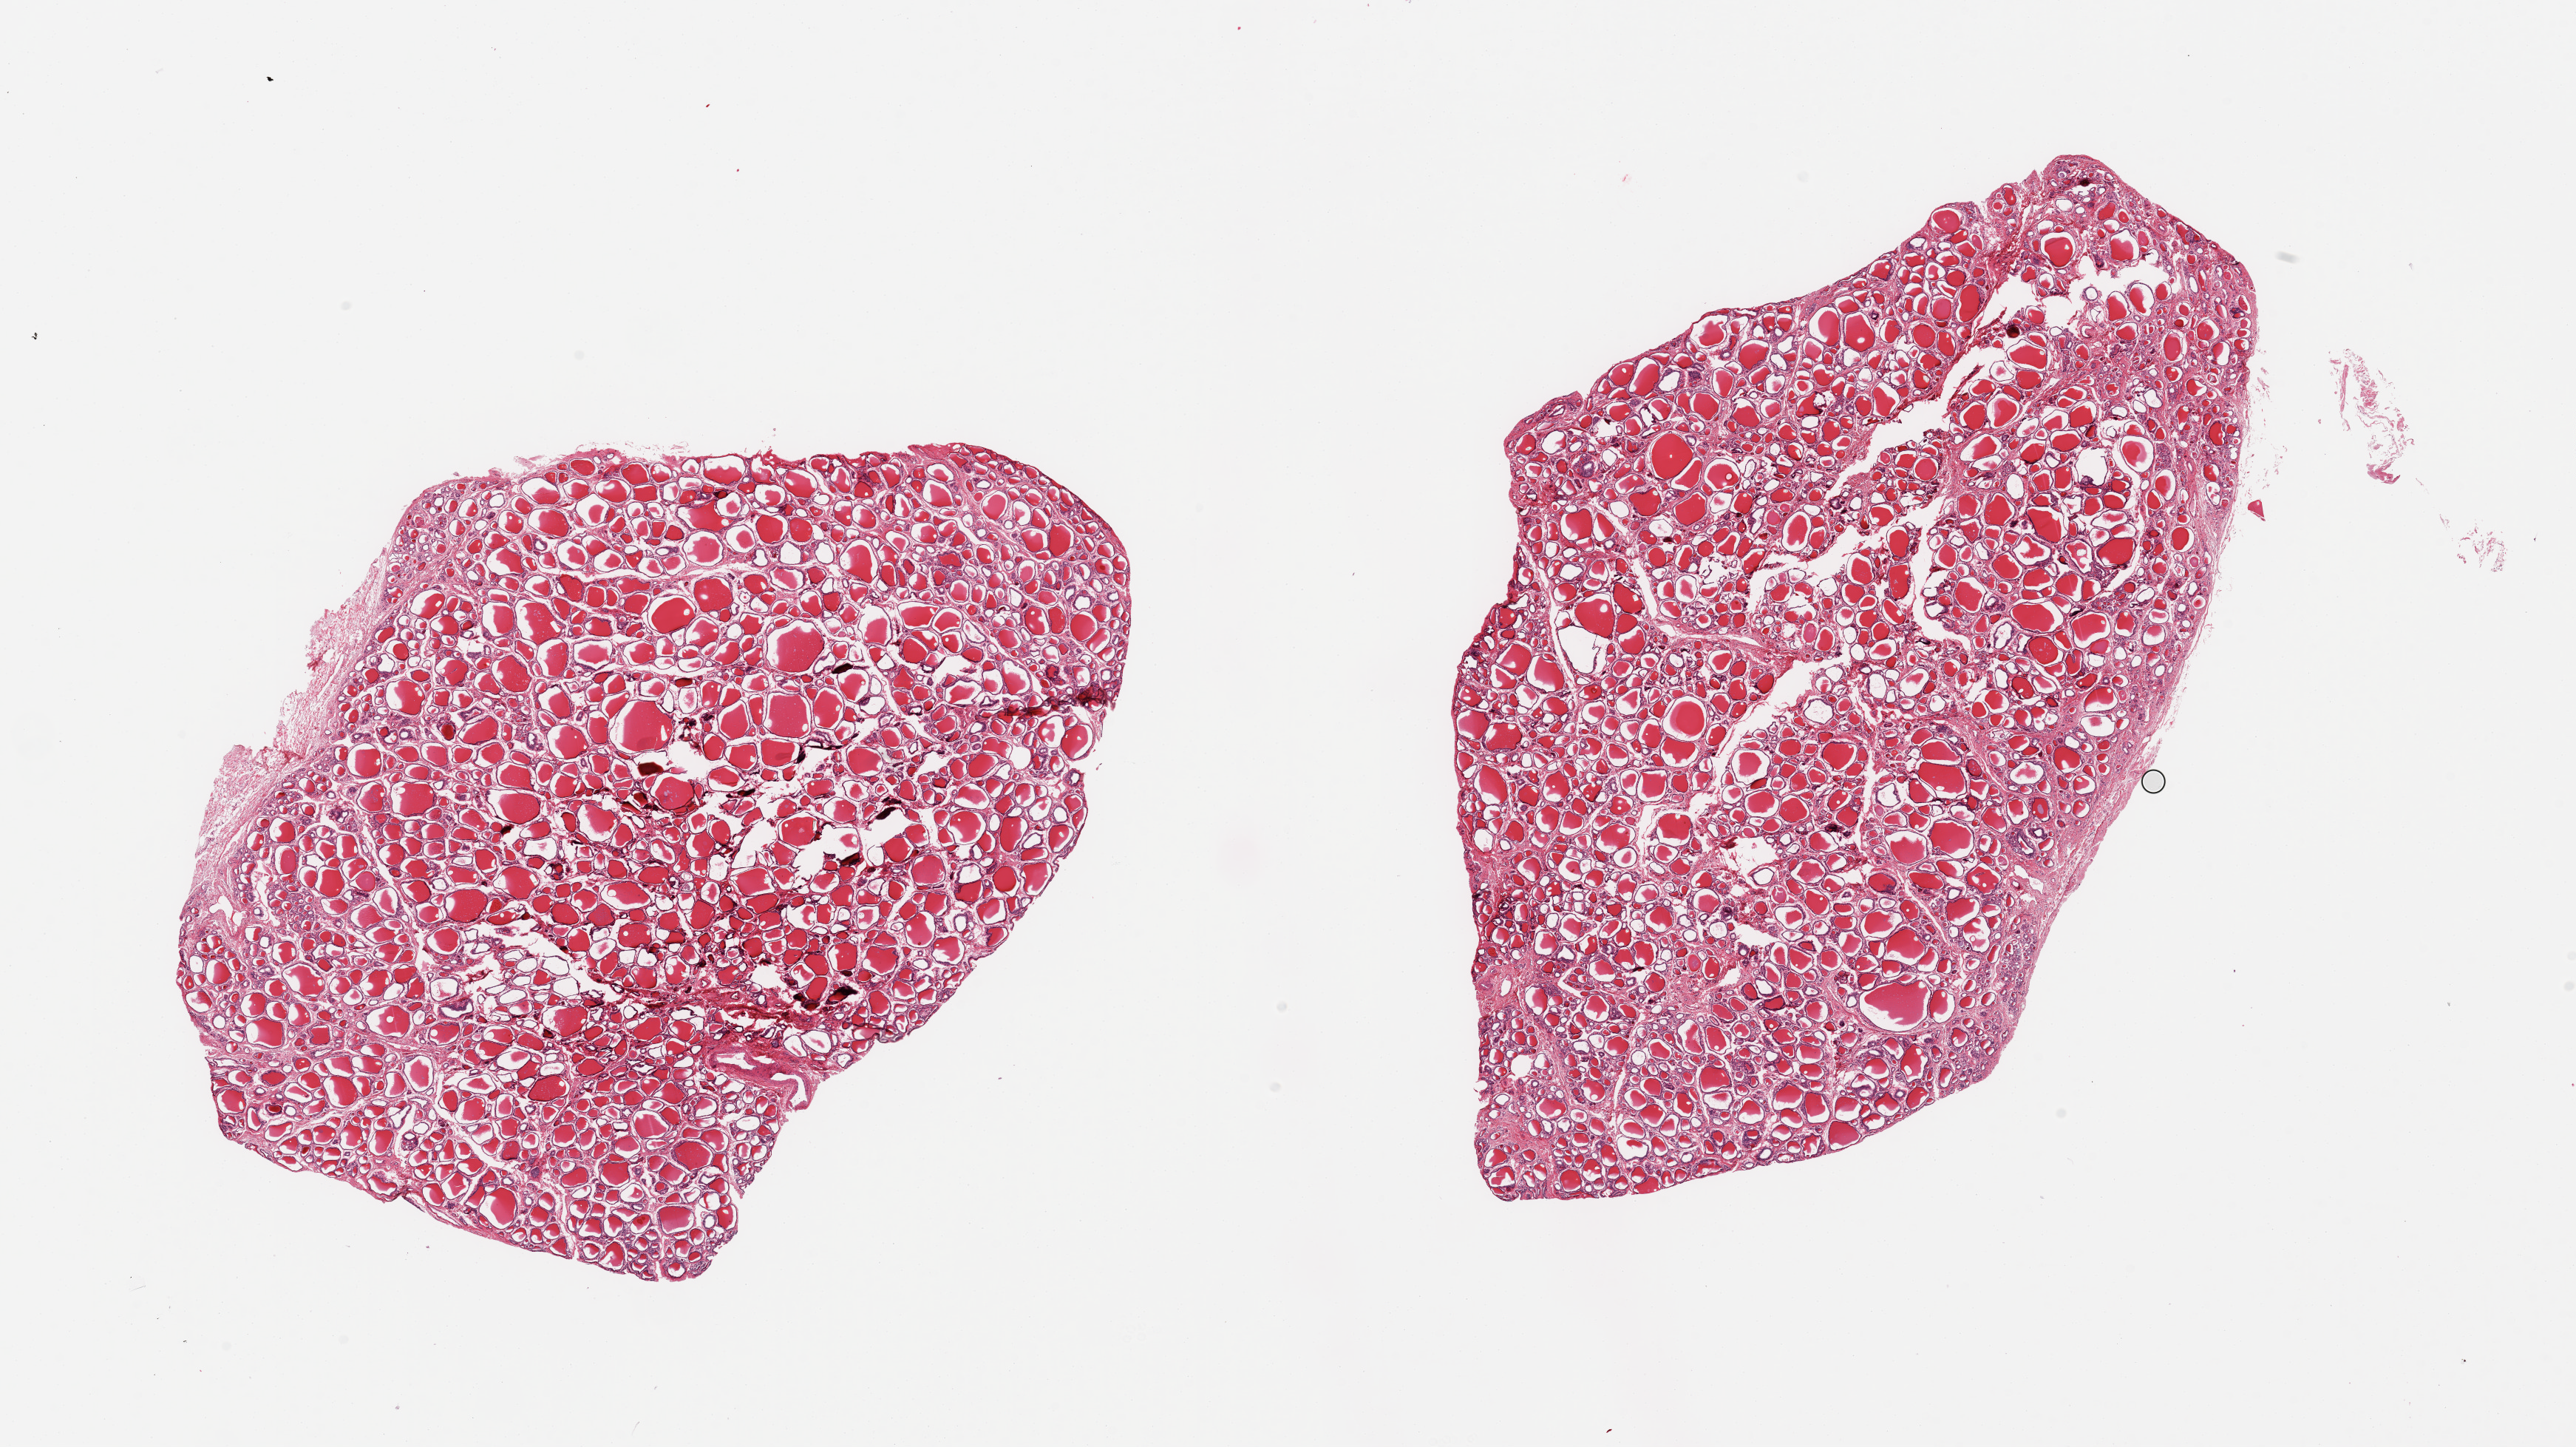
Whole-slide image, hematoxylin and eosin (H&E) stain — low-resolution overview of the scanned area, about 27.6 x 15.5 mm, PAXgene-fixed paraffin-embedded (PFPE) section, sampled site (target tissue): thyroid, tissue donor sample. Donor: male.
Reviewer comment on this tissue sample: 2 pieces, no abnormalities.